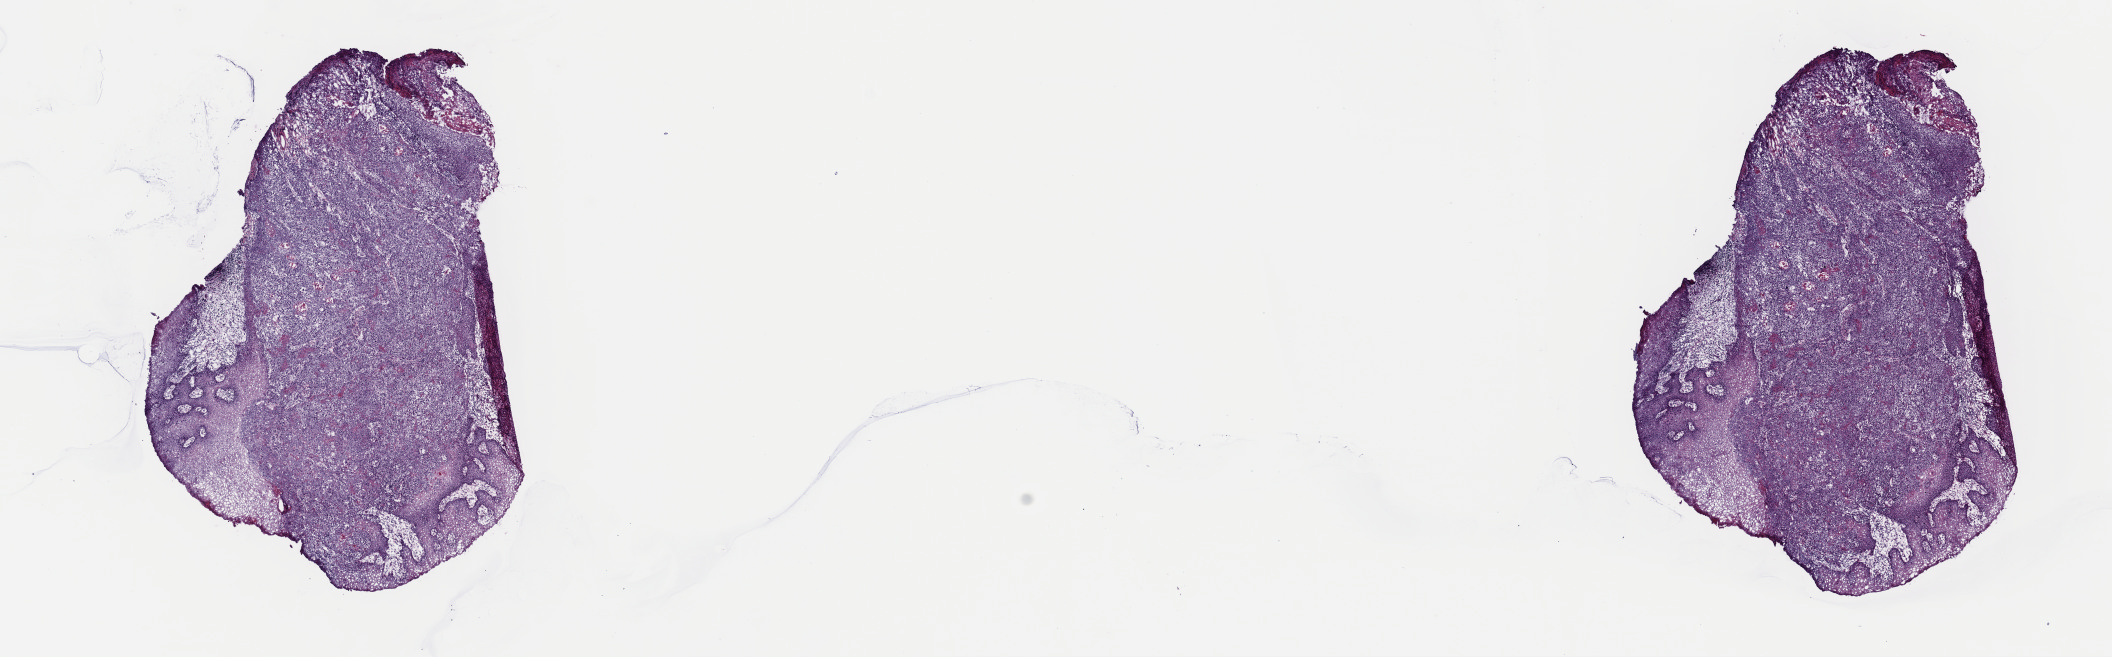
H&E-stained whole-slide image — a low-resolution overview of the entire scanned area, about 16.7 x 5.2 mm (acquisition: 40x scan), frozen section, primary tumour sample from the head and neck. Male, age 77 years at initial diagnosis. Histologic grade: G3 (poorly differentiated). Pathologist review of this section (percent, as recorded): tumour cells 90%, tumour nuclei 100%, normal cells 0%, stromal cells 10%, necrosis 0%. Infiltration values recorded for this section: lymphocyte infiltration 3%, monocyte infiltration 1%, neutrophil infiltration 1%.
• pathologic diagnosis: Squamous cell carcinoma, NOS (oropharynx, NOS)